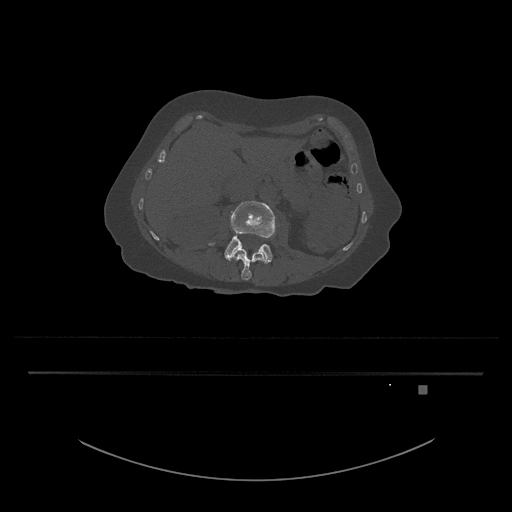
CT including the spine, one axial slice. Position 457 of 797 along the scan axis. Reconstruction kernel Br40s/3. Bone window (W 1800 / L 400 HU). 0.5 mm slice thickness. 512 × 512 image matrix, field of view 500 × 500 mm. Patient: female, 57 years. Case-level facts recorded for this patient, not image findings: primary cancer: cervical.
Structures marked on this image (semi-automatically segmented with operator editing):
- L3 vertebra: bounding box <208,201,277,264> (left, top, right, bottom; pixels)